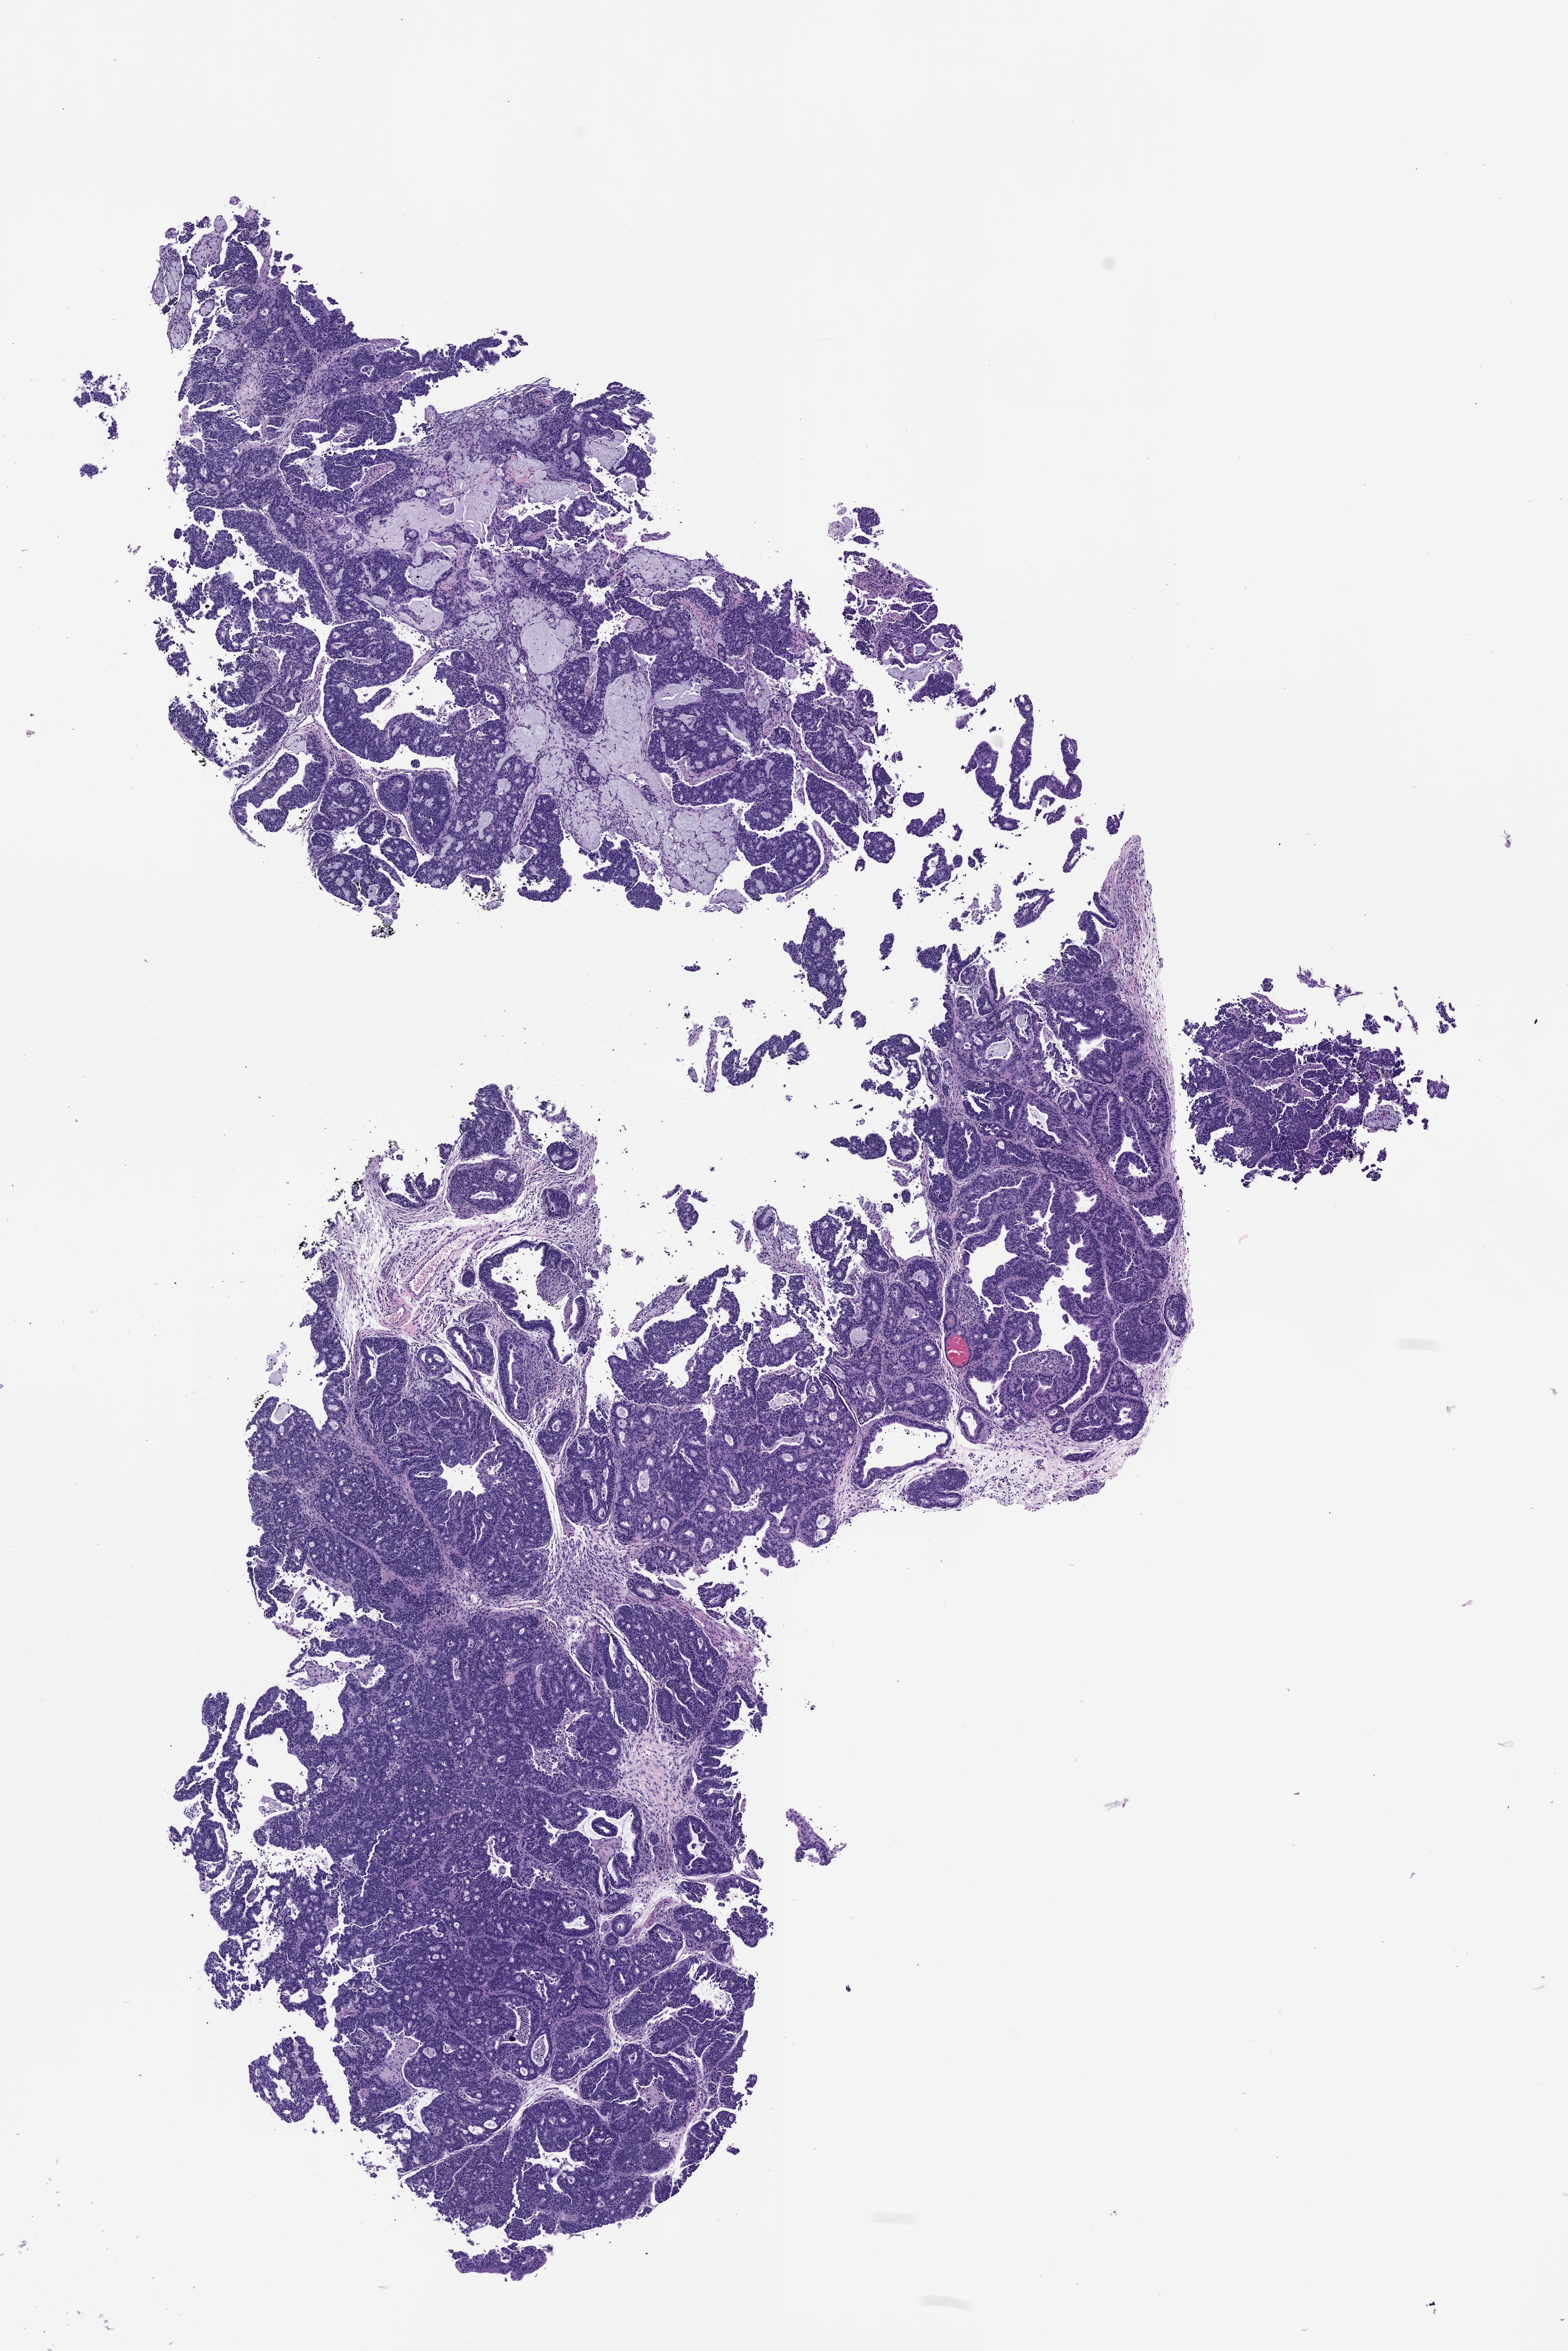
Whole-slide image, haematoxylin and eosin: patient-derived xenograft (human tumor grown in a mouse), passage 1, whole scanned area (about 8.0 x 12.0 mm) shown as a low-resolution overview, formalin-fixed, paraffin-embedded (FFPE) tissue, originating tumor site category: rectum.
- originating patient diagnosis: Rectal Adenocarcinoma